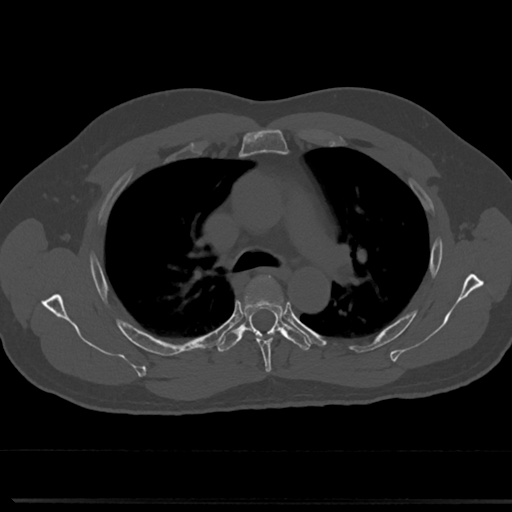
CT including the spine, one axial slice. Position 519 of 817 along the scan axis. Reconstruction kernel Br40s/3. 120 kVp. Bone window (W 1800 / L 400 HU). 512 × 512 image matrix. Patient: male, 61 years. From the clinical record (not read from this slice): primary cancer: prostate.
Annotated regions visible in this slice (semi-automatically segmented with operator editing):
- T4 vertebra: box from (x=241, y=275) to (x=287, y=363) px
- T5 vertebra: (x=221, y=306)–(x=310, y=349)